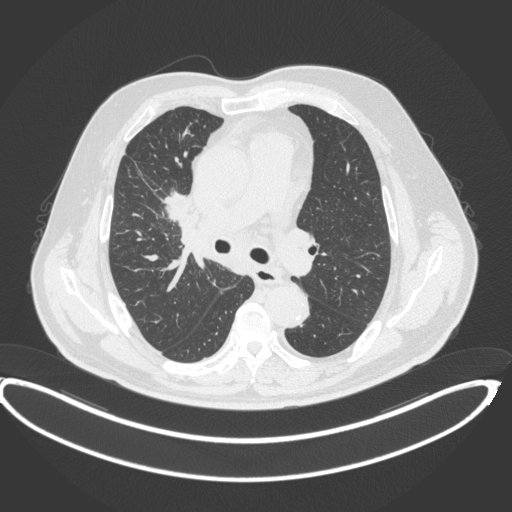
Chest CT, one axial slice. Position 251 of 395 along the scan axis. 120 kVp. Lung window (W 1500 / L -600 HU). 512 × 512 image matrix, field of view 448 × 448 mm. Patient: male, 62 years. Case-level facts recorded for this patient, not image findings: clinical TNM (as recorded): T1c N3 M1c.
Outlined on this slice (bounding box drawn by a radiologist):
- lung tumour (recorded histology: adenocarcinoma): bounding box [x1, y1, x2, y2] px = [161, 186, 201, 230]